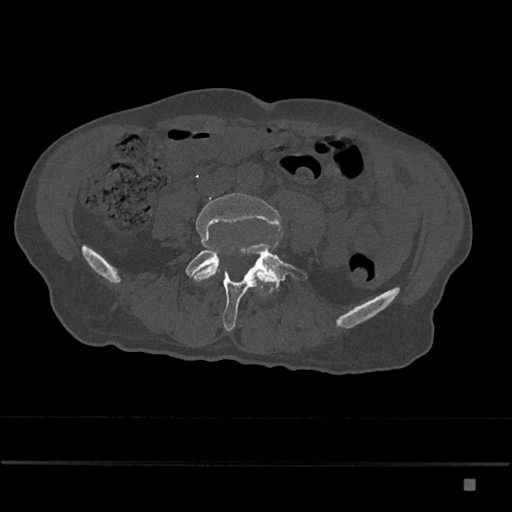
CT including the spine, one axial slice; bone window (W 1800 / L 400 HU); 0.5 mm slice thickness; 512 × 512 image matrix, field of view 390 × 390 mm. Patient: male, 72 years. Case-level facts recorded for this patient, not image findings: primary cancer: prostate.
Outlined on this slice (semi-automatically segmented with operator editing):
- L4 vertebra: bounding box (x1, y1, x2, y2) in pixels: (190, 193, 282, 282)
- L5 vertebra: (185, 244, 307, 332)